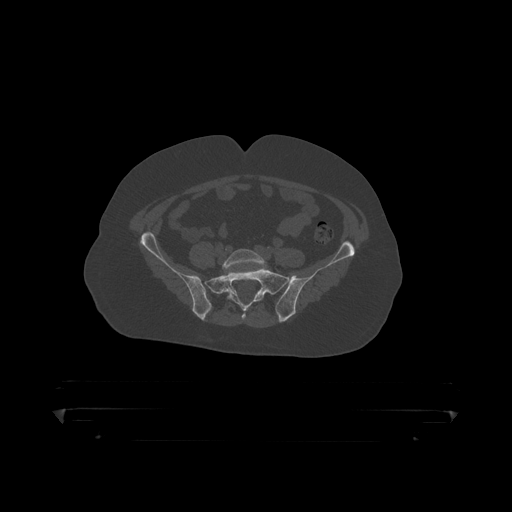
CT including the spine, one axial slice. Position 24 of 390 along the scan axis. Bone window (W 1800 / L 400 HU). 1.25 mm slice thickness. 512 × 512 image matrix, field of view 650 × 650 mm. Male patient, age 60 years. From the clinical record (not read from this slice): primary cancer: prostate.
Structures marked on this image (semi-automatically segmented with operator editing):
- L5 vertebra: bounding box <223,249,267,293> (left, top, right, bottom; pixels)